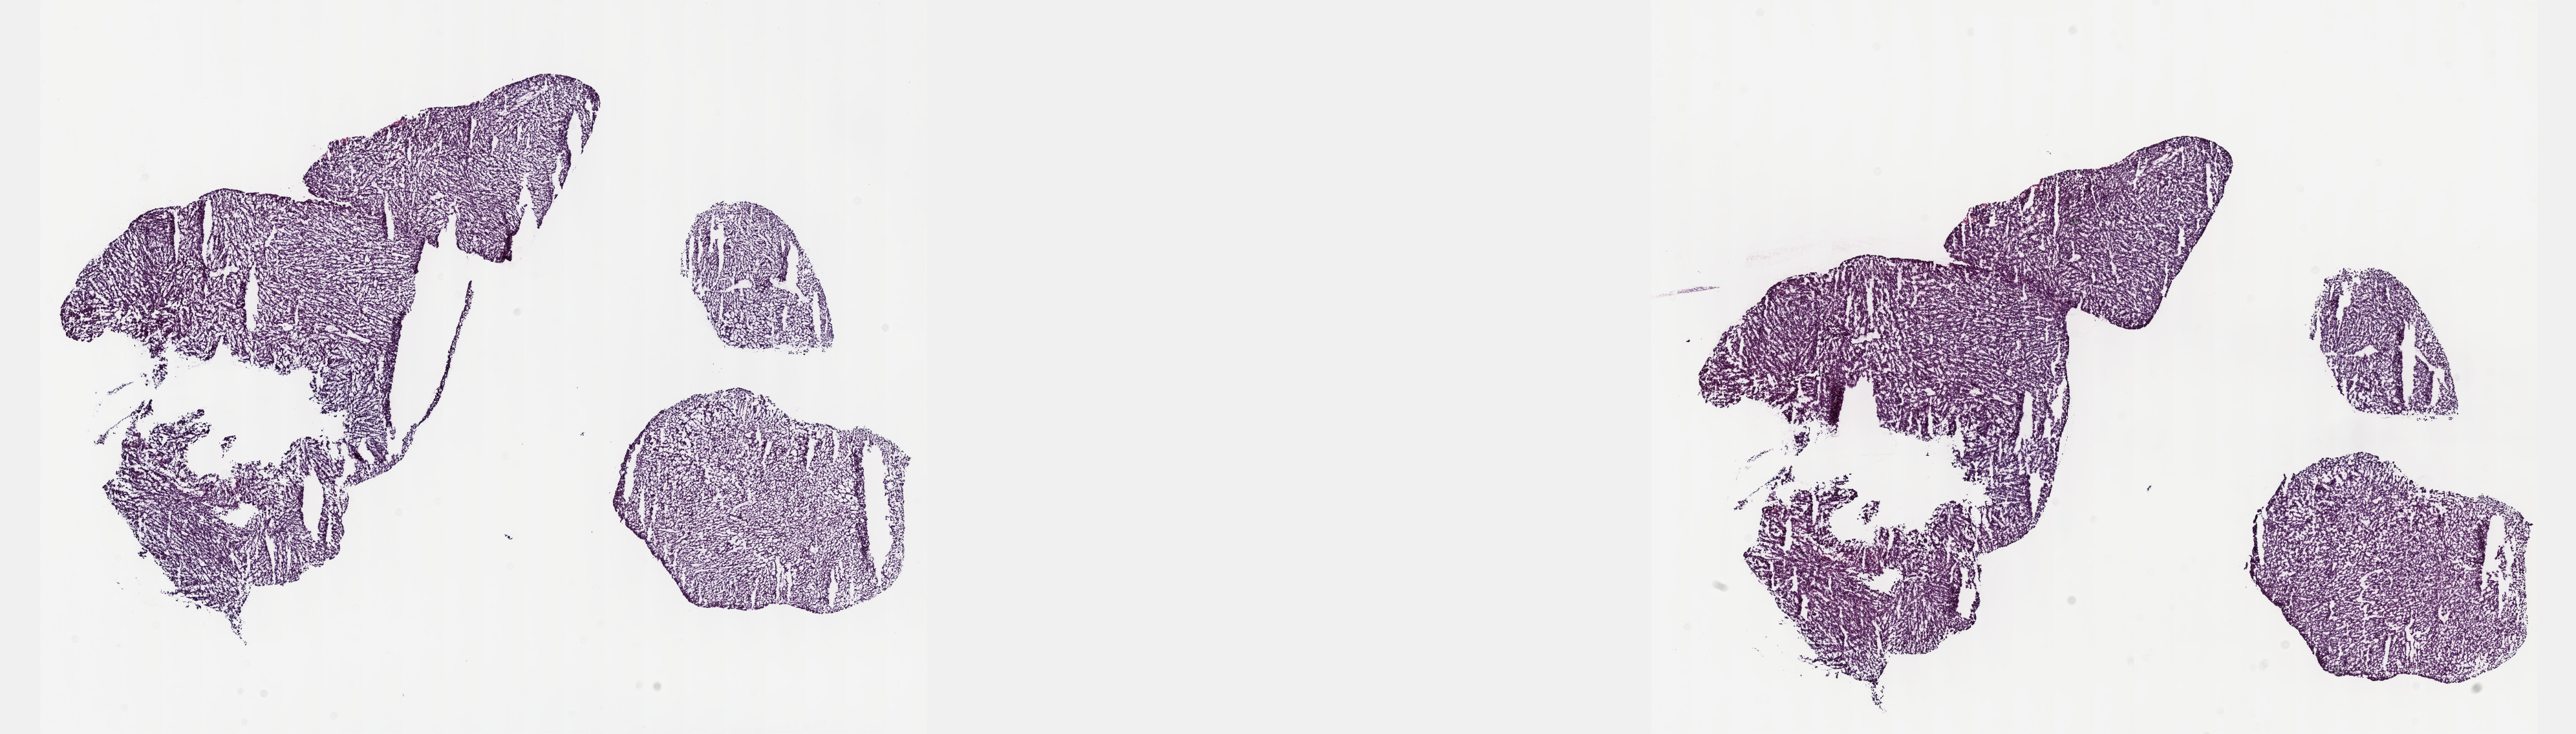
H&E-stained whole-slide image — a low-resolution overview of the entire scanned area, about 32.2 x 9.2 mm (from a 40x scan), frozen section, liver, primary tumour sample. Female patient; age at initial diagnosis 59 years. Histologic grade: G2 (moderately differentiated). Composition of this section per pathologist review: tumour cells 94%, tumour nuclei 97%, normal cells 0%, stromal cells 1%, necrosis 5%. Infiltration values recorded for this section: lymphocyte infiltration 1%, monocyte infiltration 1%, neutrophil infiltration 0%.
Histologic diagnosis: Hepatocellular carcinoma, NOS. AJCC pathologic stage: I (7th edition).